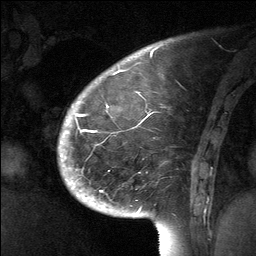
Breast MRI (dynamic contrast-enhanced), one sagittal slice; position 17 of 64 along the scan axis; dynamic contrast-enhanced study with each time point stored as its own series, time point 2 of 3 at this slice position (early post-contrast, ordered by acquisition time); 1.5 T; TE 4.8 ms, TR 27 ms; 2 mm slice thickness; 256 × 256 image matrix. Female patient, age 39 years. Case-level facts recorded for this patient, not image findings: setting: breast cancer imaged before/during neoadjuvant chemotherapy; receptor status: HER2-positive.
Structures marked on this image (semi-automatically segmented with operator editing):
- analysis volume of interest (the breast-tissue region the enhancement analysis was run in; not a lesion): bounding box [x1, y1, x2, y2] px = [70, 69, 202, 224]
- tumour enhancement mask (voxels above the 90 % enhancement threshold inside the analysis volume of interest): [77, 106, 108, 132]